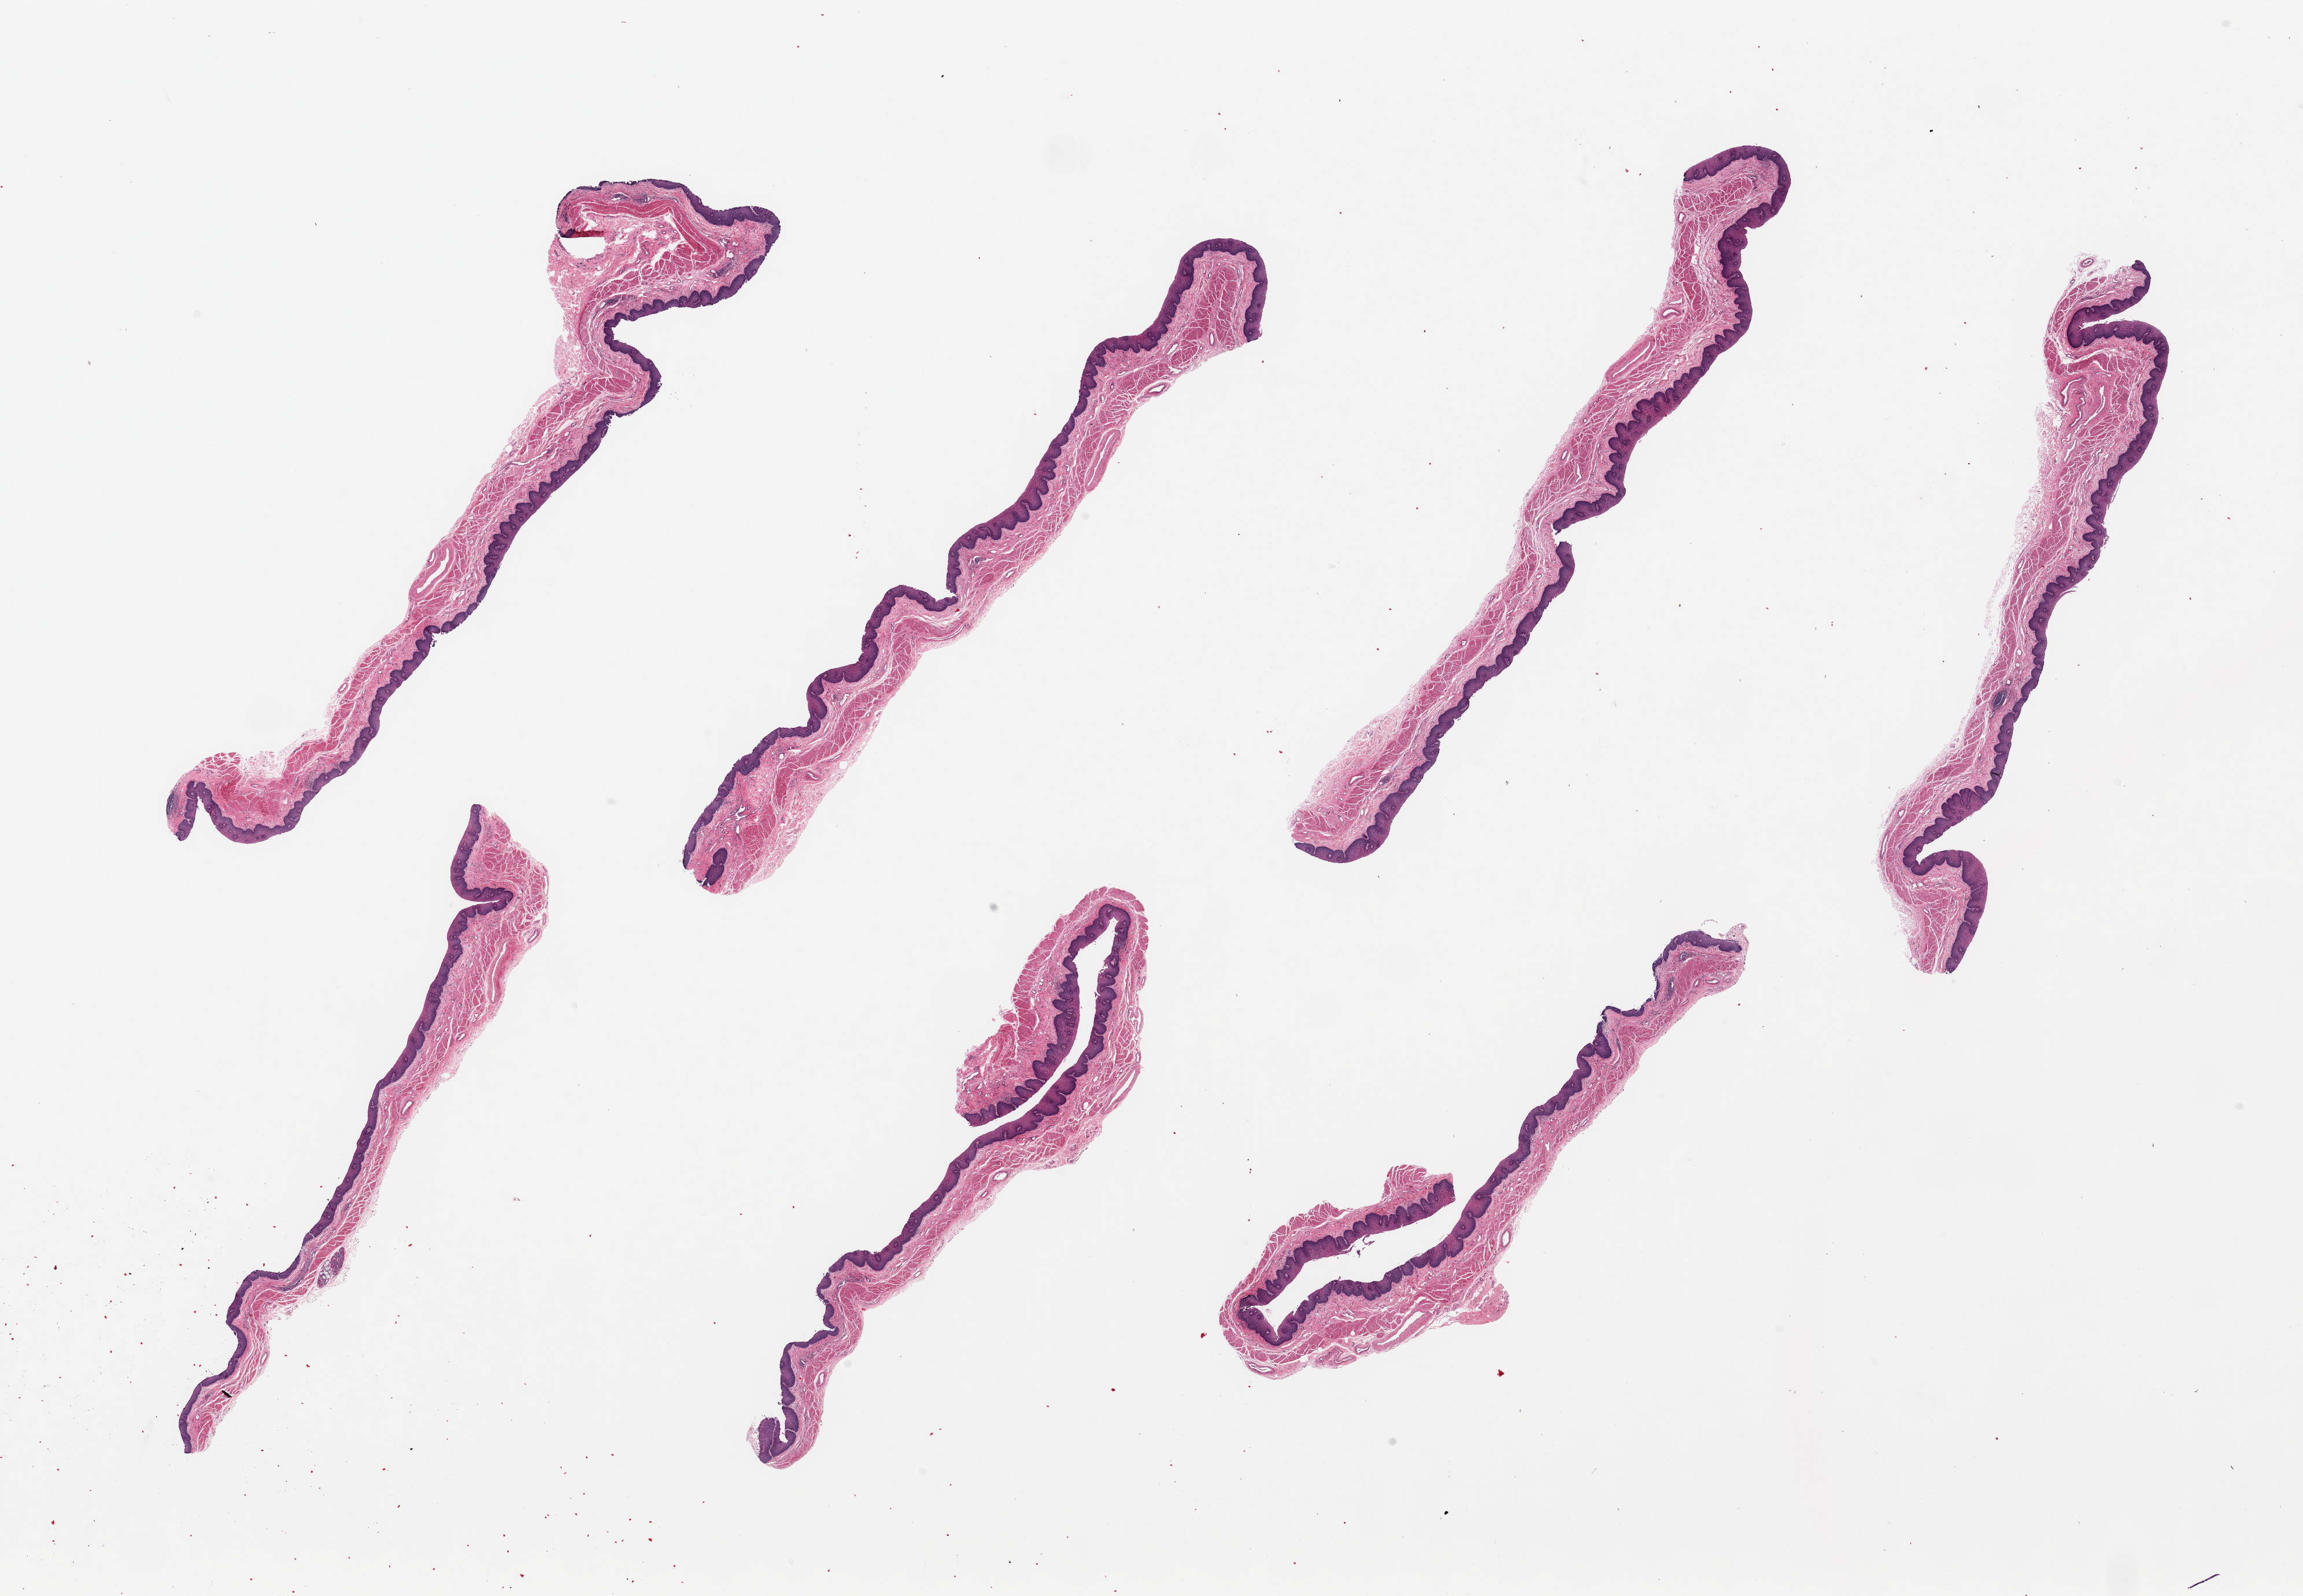
Haematoxylin and eosin whole-slide image, brightfield, low-resolution overview of the scanned area, about 31.5 x 21.8 mm, PAXgene-fixed paraffin-embedded (PFPE) section, section of esophageal mucous membrane (target tissue), tissue donor sample. Donor: male.
Pathologist's review note for this sample: 7 pieces ~10x1mm. Squamous mucosa is 20-30% thickness.